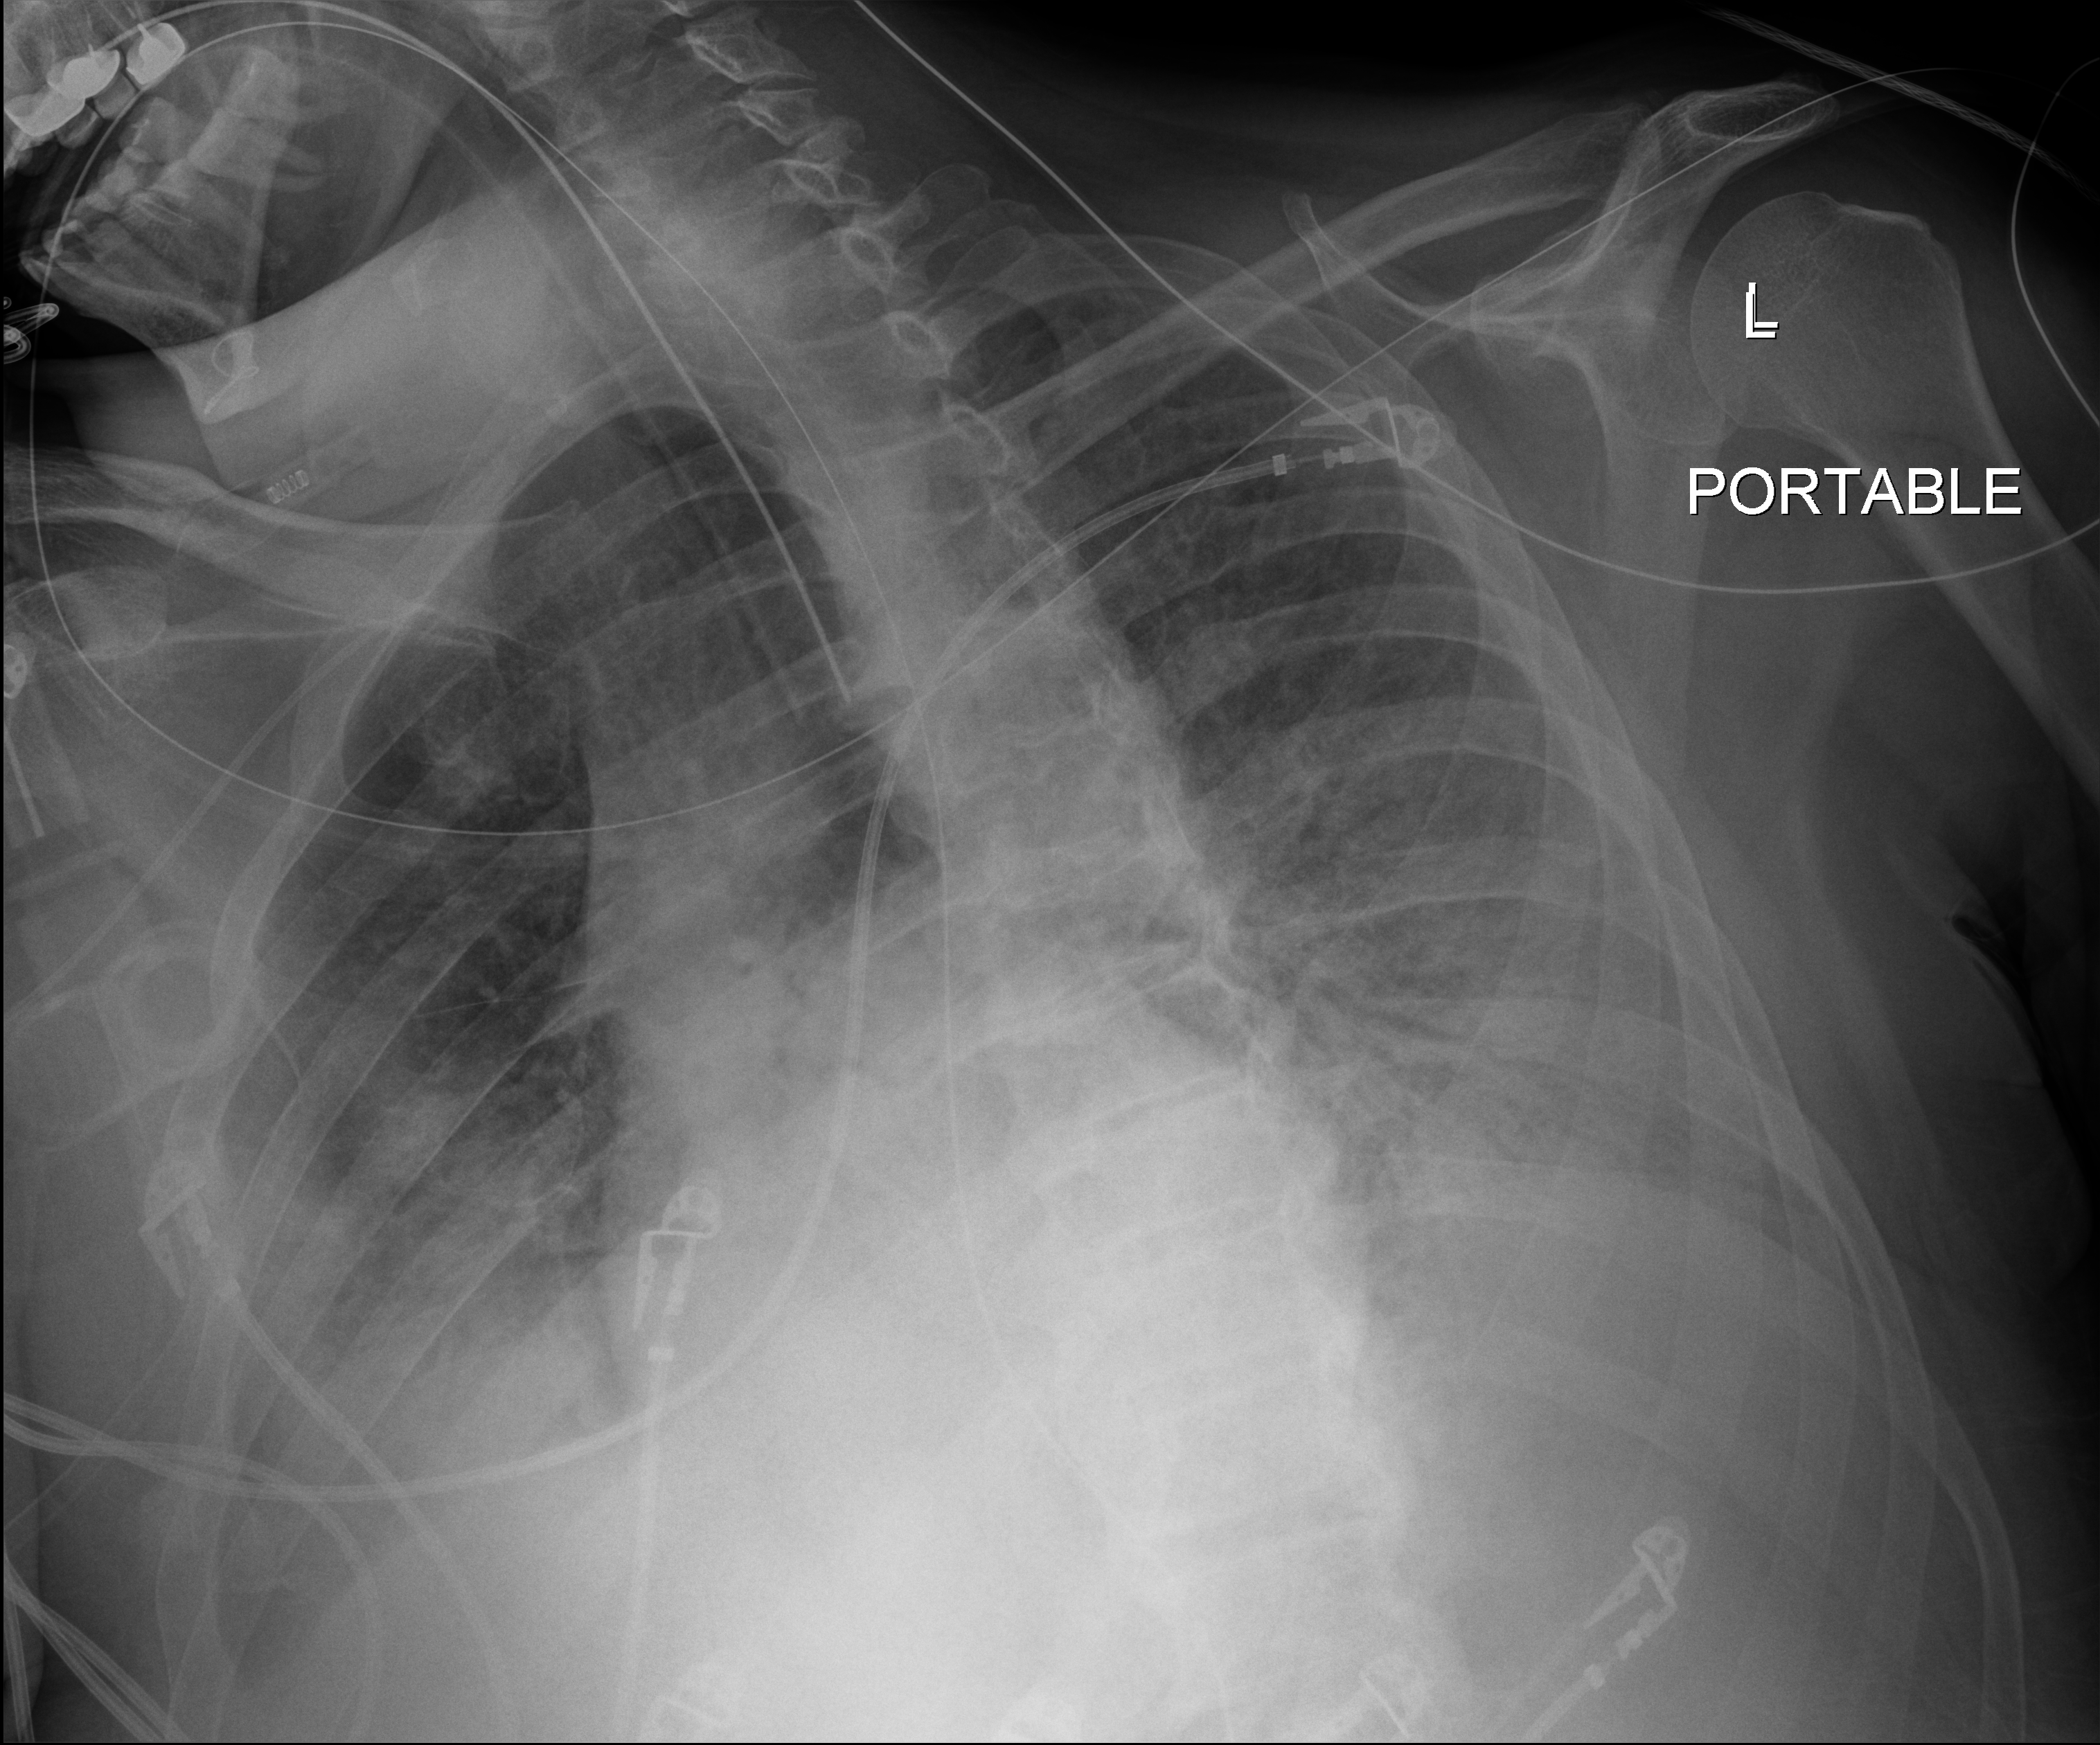
Portable chest radiograph. Male patient hospitalised with COVID-19, age 60–74 years.
From the hospital-stay record, not from the radiograph (when in the stay this image was taken is not recorded):
- admitted to intensive care during this hospital stay: yes